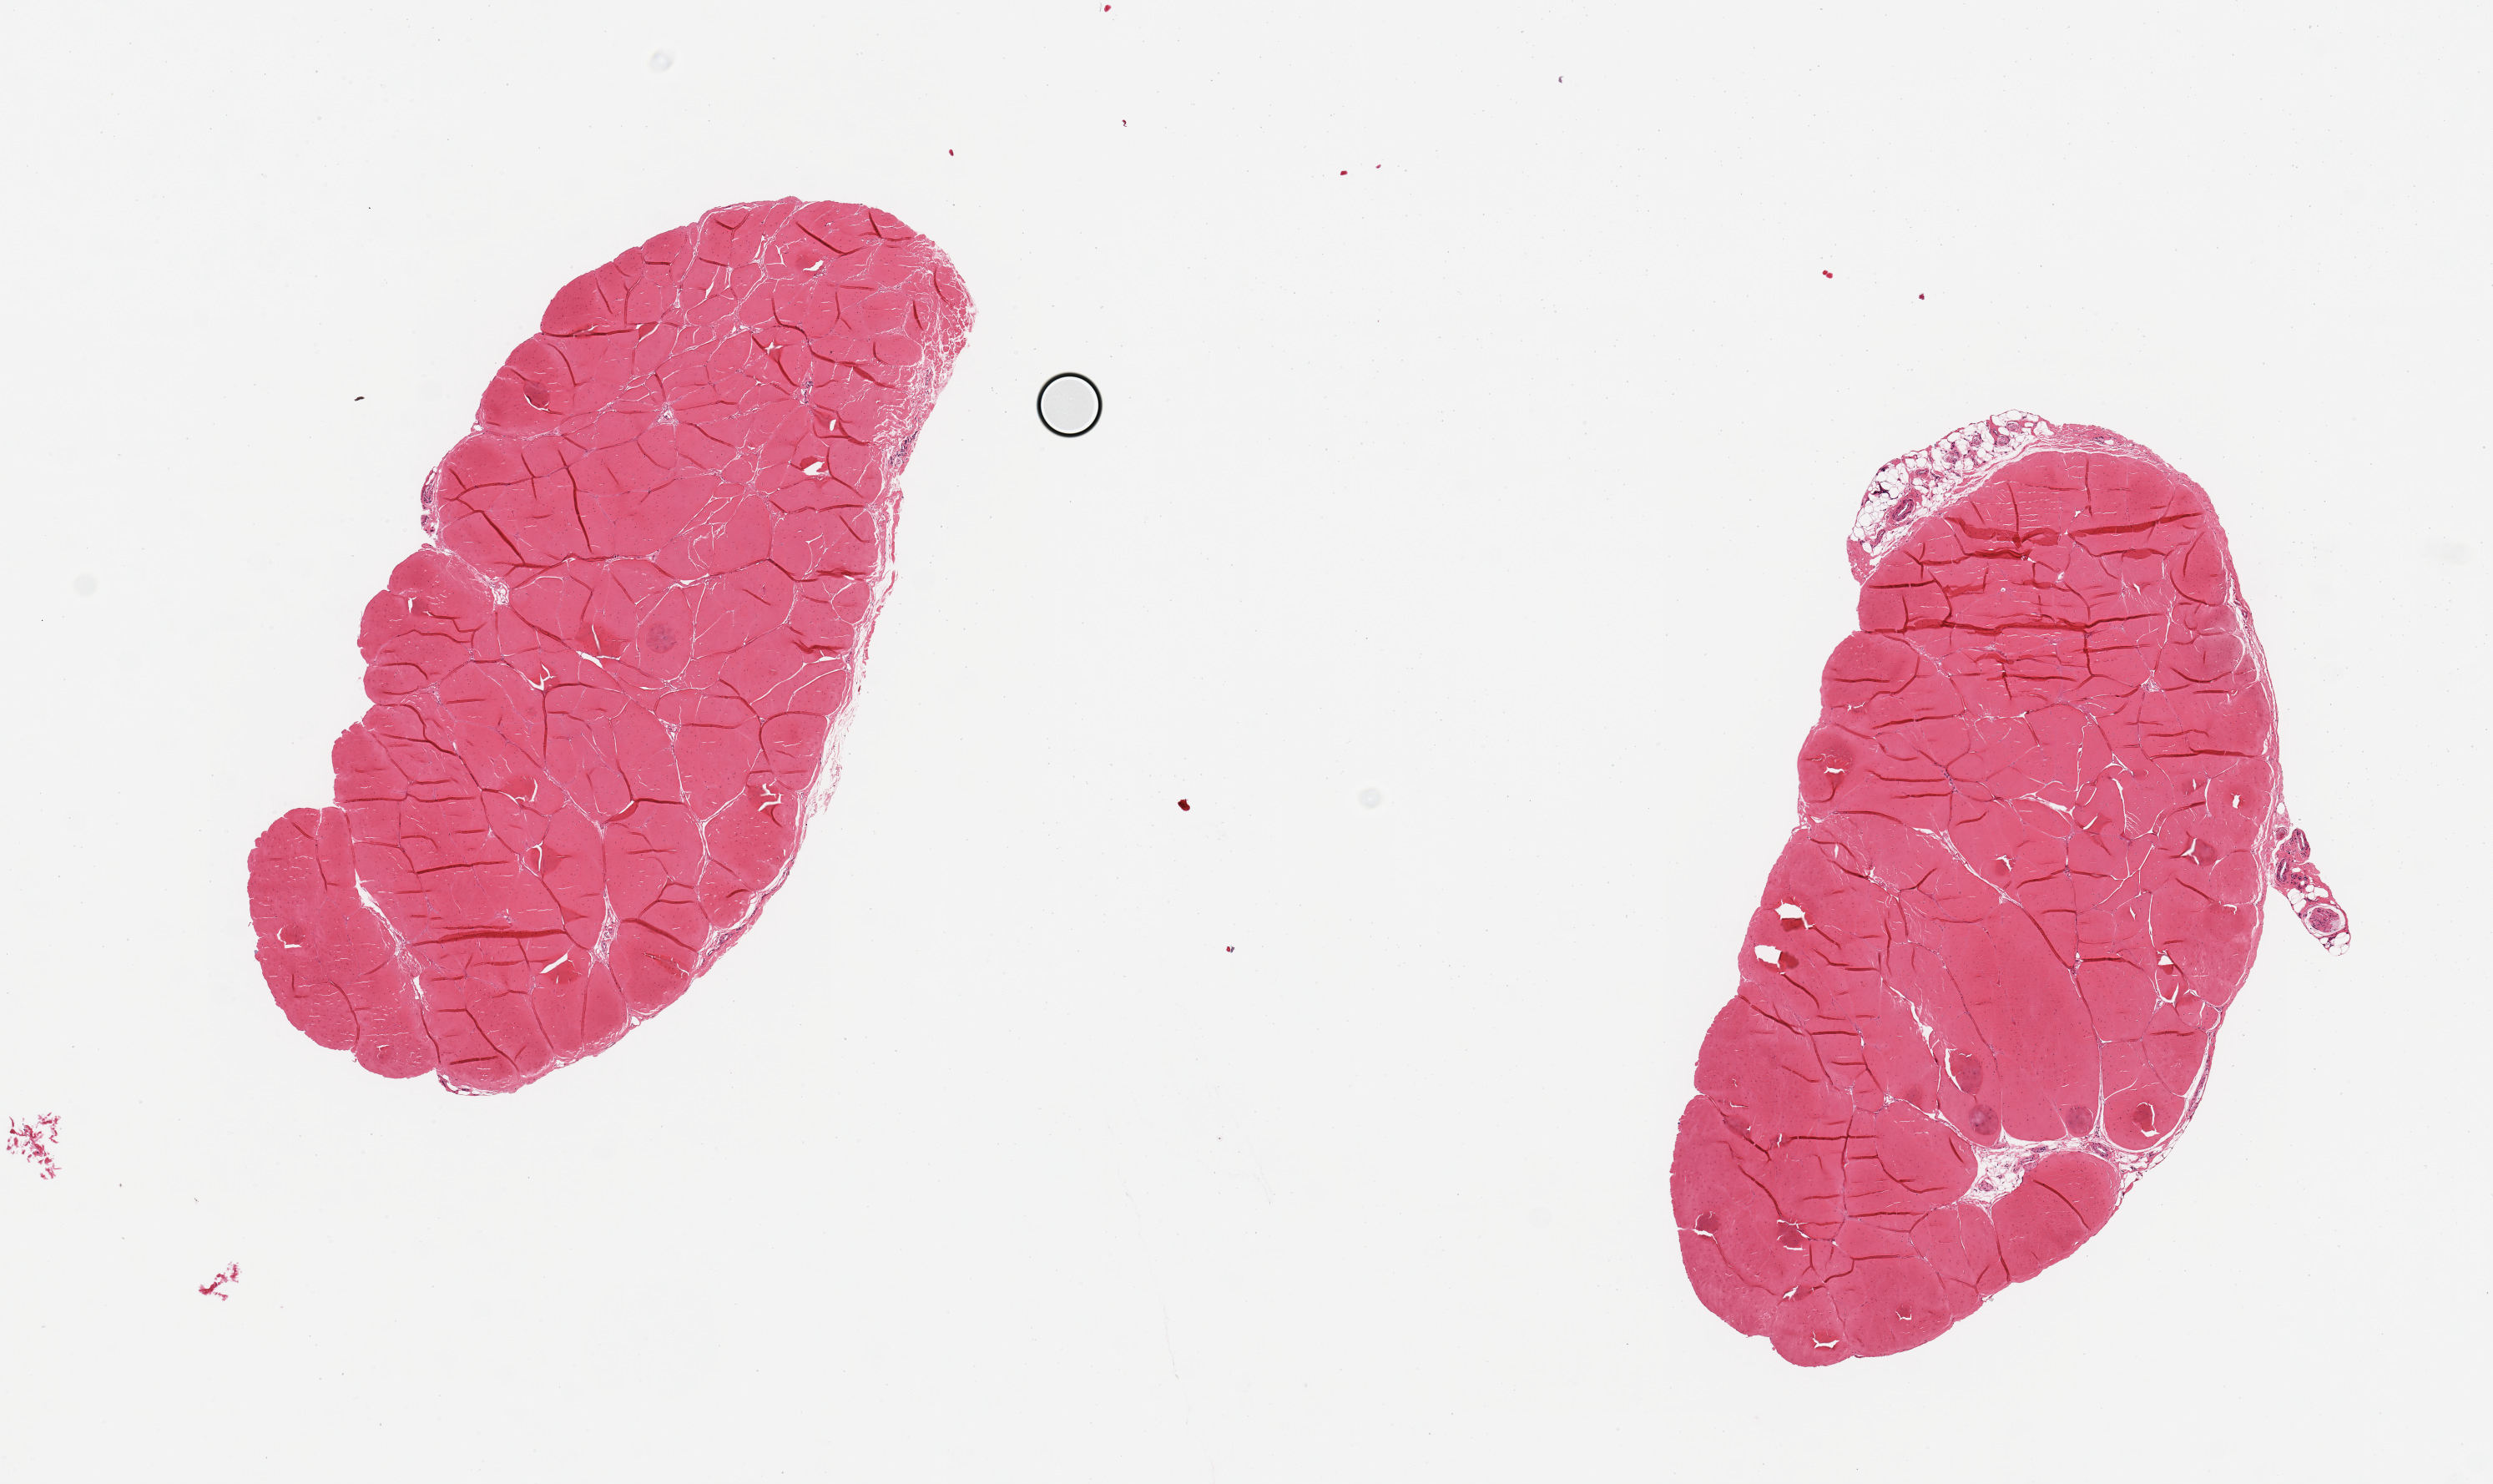
H&E whole-slide image, brightfield, a low-resolution overview of the entire scanned area, about 11.8 x 7.0 mm, PAXgene-fixed paraffin-embedded (PFPE) section, section of tibial nerve (target tissue), tissue donor sample.
Pathologist's review note for this sample: 2 pieces of tendon, incorrect tissue.